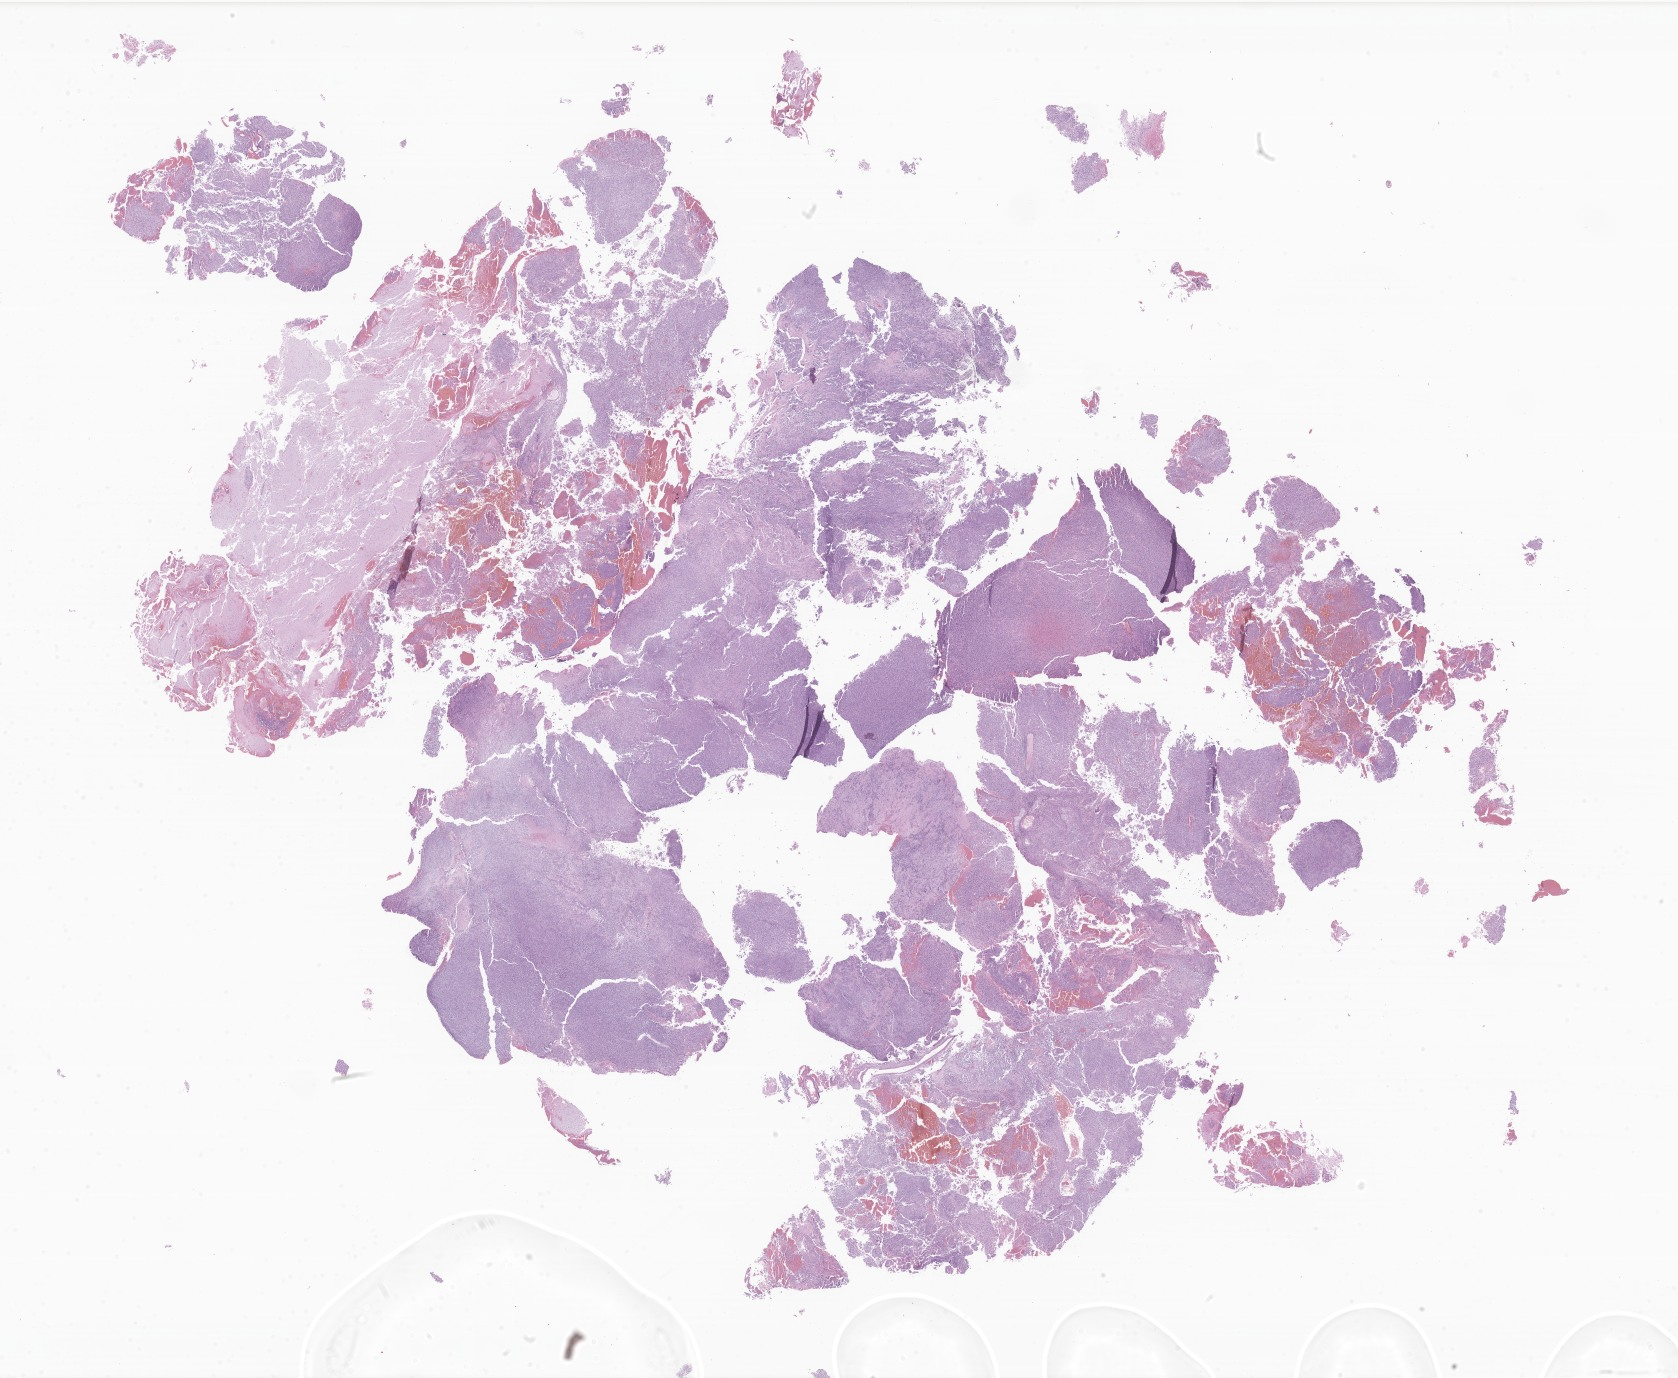
Hematoxylin and eosin (H&E) whole-slide image of tumor tissue from the brain, shown as a low-resolution overview of the whole scanned area (about 28.3 x 23.2 mm); formalin-fixed paraffin-embedded section. Patient: female, age 980 days (about 2.7 years).
Diagnosis (ICD-O-3 morphology term): Atypical teratoid/rhabdoid tumor.